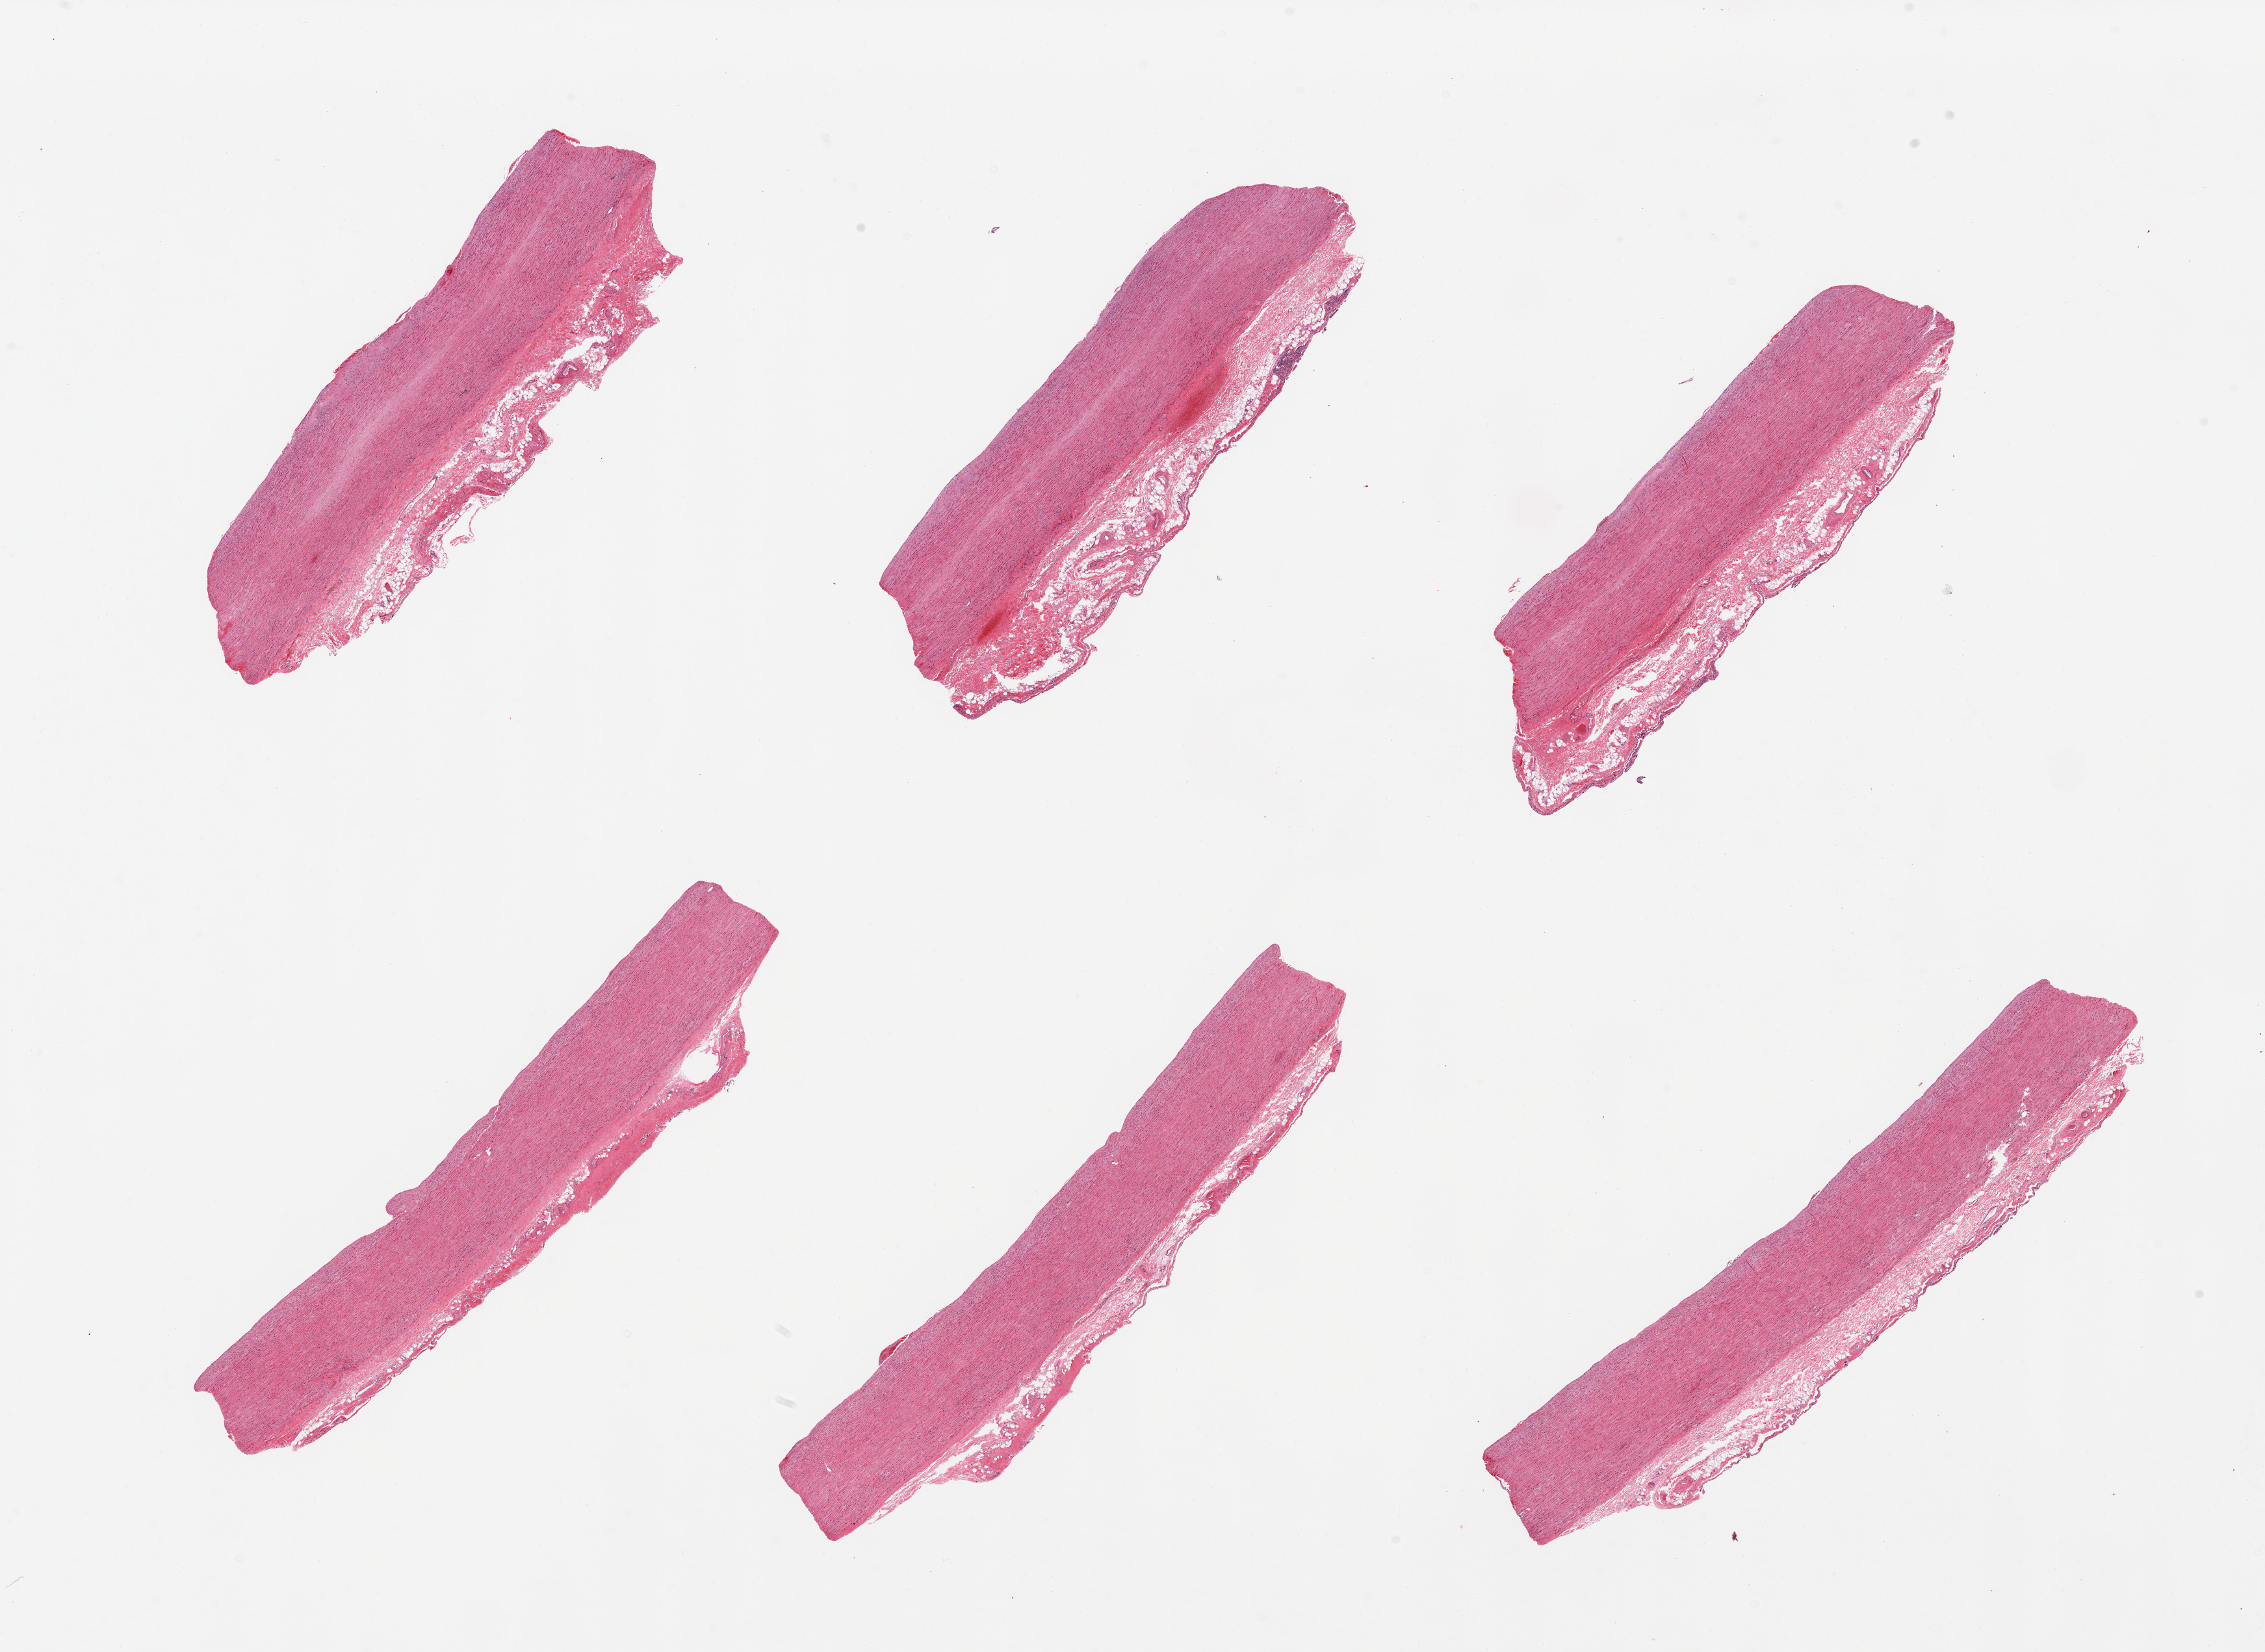
Whole-slide image, hematoxylin and eosin (H&E) stain — a low-resolution overview of the entire scanned area, about 27.6 x 20.1 mm (slide scanned at 20x), PAXgene-fixed paraffin-embedded (PFPE) section, section of aorta (target tissue), tissue donor sample.
Reviewer comment on this tissue sample: 6 pieces, intimal thickening, attached adventitia with fat, nerve, and focal collection of lymphocytes.